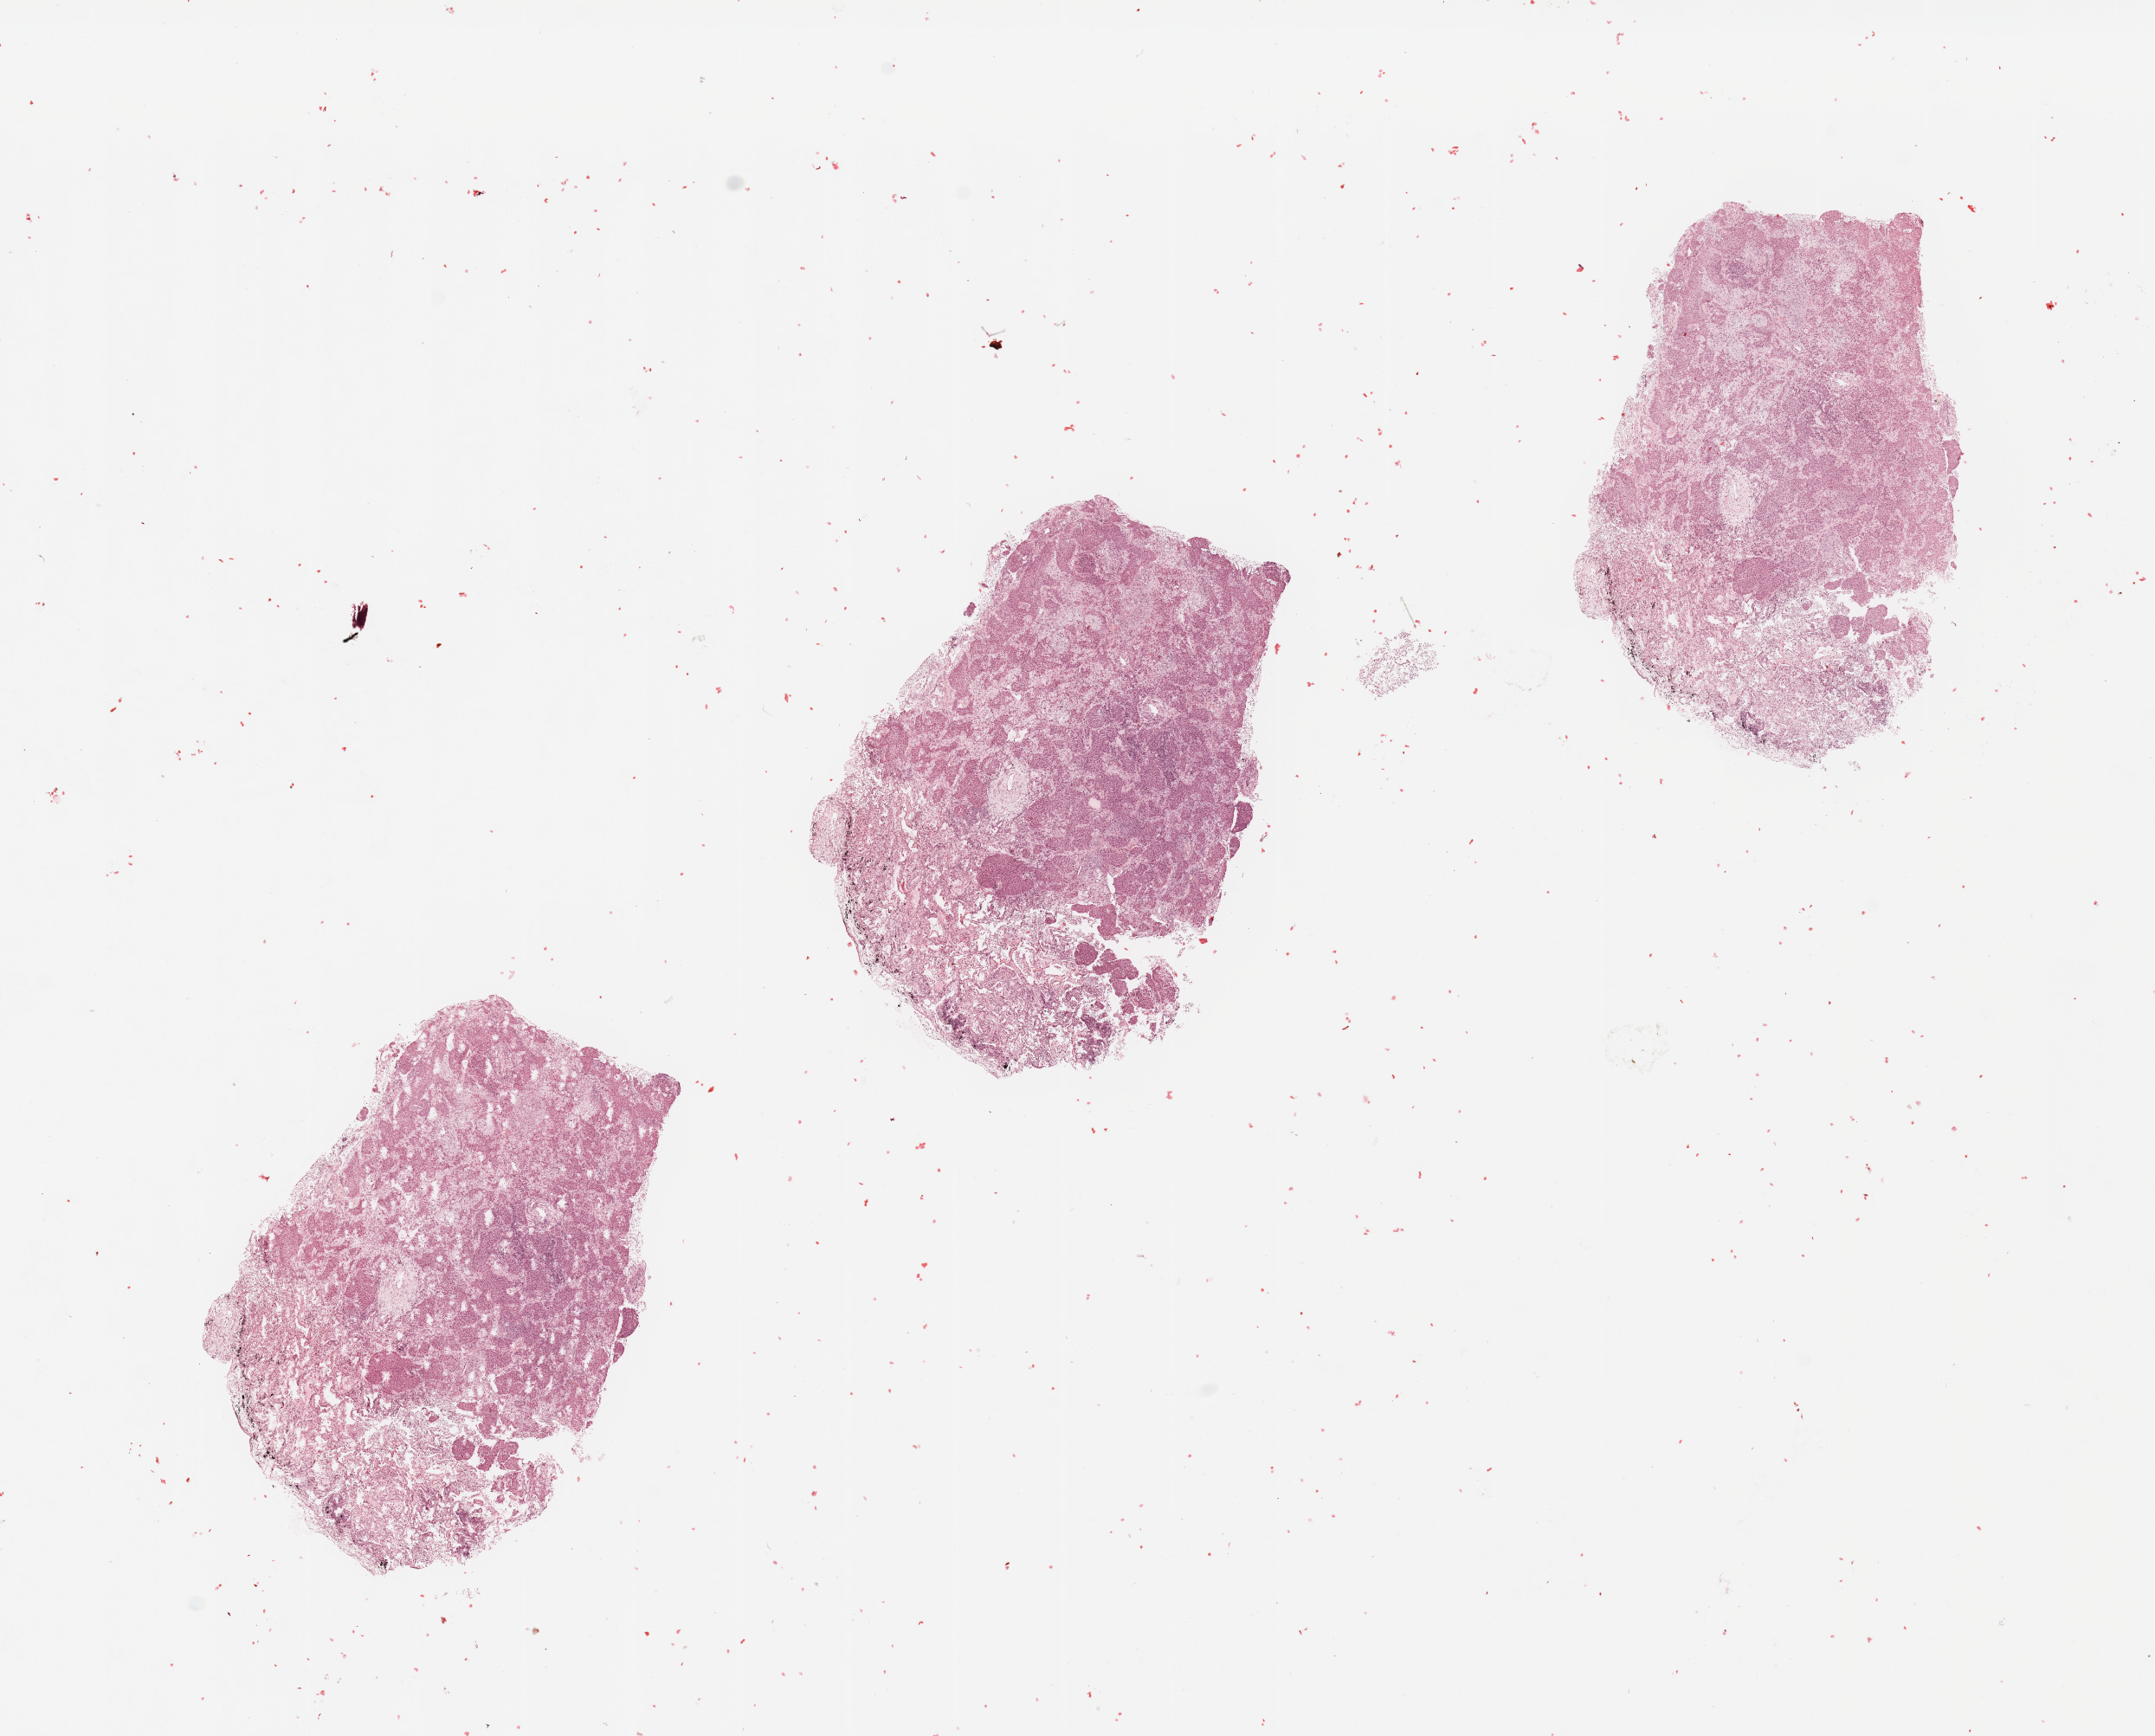
Whole-slide histology image, H&E, a low-resolution overview of the entire scanned area, about 19.7 x 15.9 mm, tumour tissue sample, sampled site: lung. 69-year-old female patient.
Diagnosis: Squamous cell carcinoma, NOS.